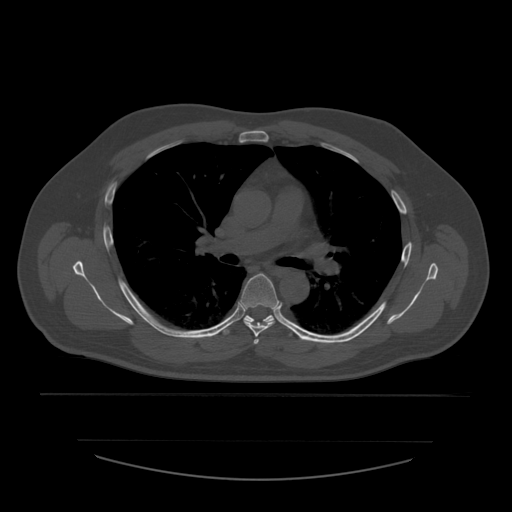
CT including the spine, one axial slice; slice 392 of 532 in the series (ordered by position); reconstruction kernel STANDARD; bone window (W 1800 / L 400 HU); 1.25 mm slice thickness; 512 × 512 image matrix. Patient age 44 years. From the clinical record (not read from this slice): primary cancer: soft tissue sarcoma.
Outlined on this slice (semi-automatic segmentation, software-assisted and operator-edited):
- T4 vertebra: bounding box [x1, y1, x2, y2] px = [254, 339, 259, 345]
- T5 vertebra: [241, 274, 280, 337]
- T6 vertebra: [221, 315, 295, 336]